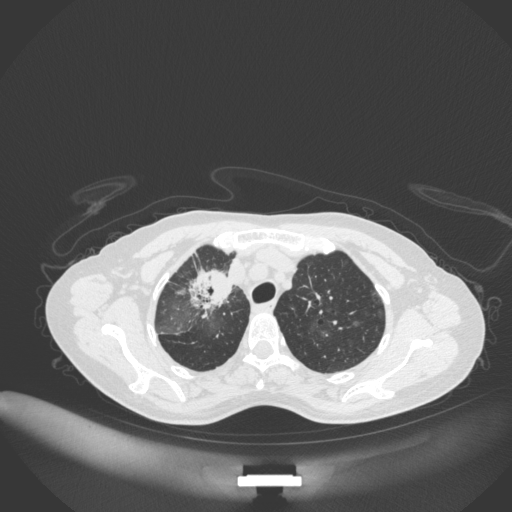
Chest CT, one axial slice; slice 259 of 311 in the series (ordered by position); reconstruction kernel B31f; 120 kVp; lung window (W 1500 / L -600 HU); 1 mm slice thickness; 512 × 512 image matrix, field of view 400 × 400 mm. Female patient, age 59 years. Case-level facts recorded for this patient, not image findings: clinical TNM (as recorded): T3 N0 M0; histopathological grade: G1.
Outlined on this slice (rectangle marked by the reading radiologist):
- lung tumour (recorded histology: adenocarcinoma): bounding box [x1, y1, x2, y2] px = [190, 261, 235, 319]